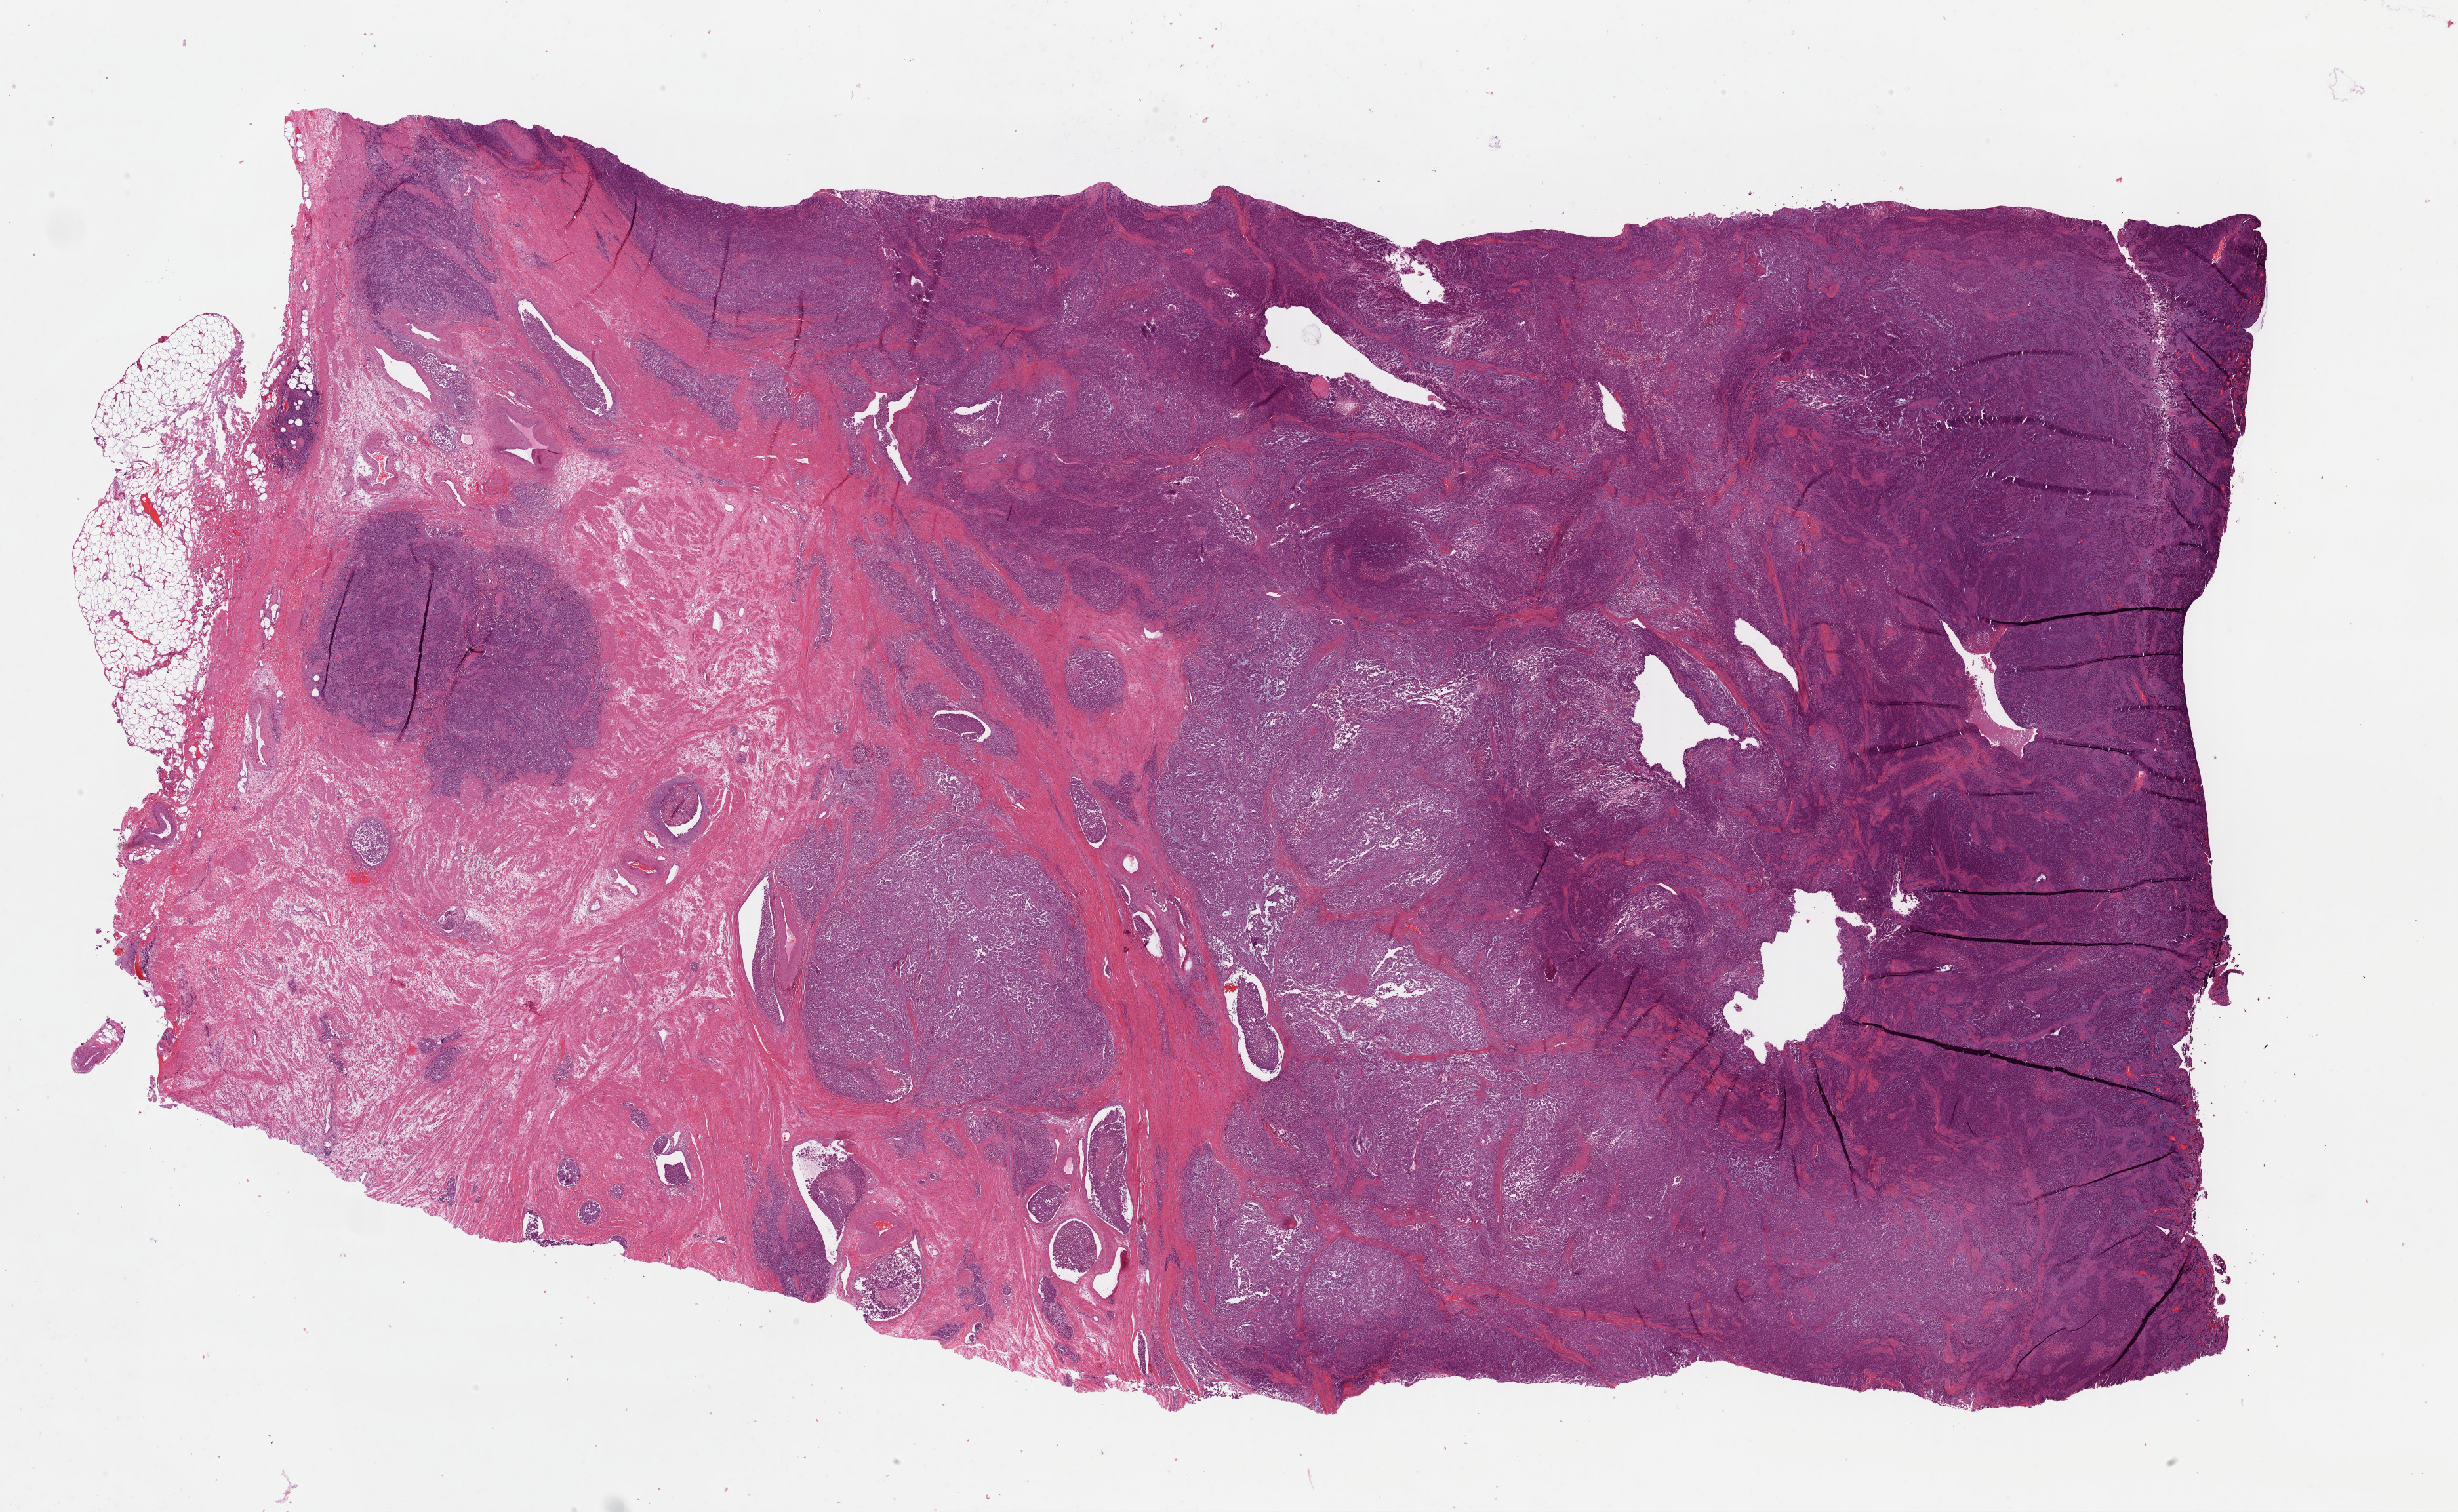
H&E whole-slide image, shown as a low-resolution overview of the whole scanned area (about 29.6 x 18.2 mm); formalin-fixed paraffin-embedded (FFPE) diagnostic section; sample: primary tumour, uterus. Patient: female, age at initial diagnosis 44 years. Histologic grade: G3 (poorly differentiated).
FIGO stage: IIIC. Histologic diagnosis: Endometrioid adenocarcinoma, NOS (endometrium).